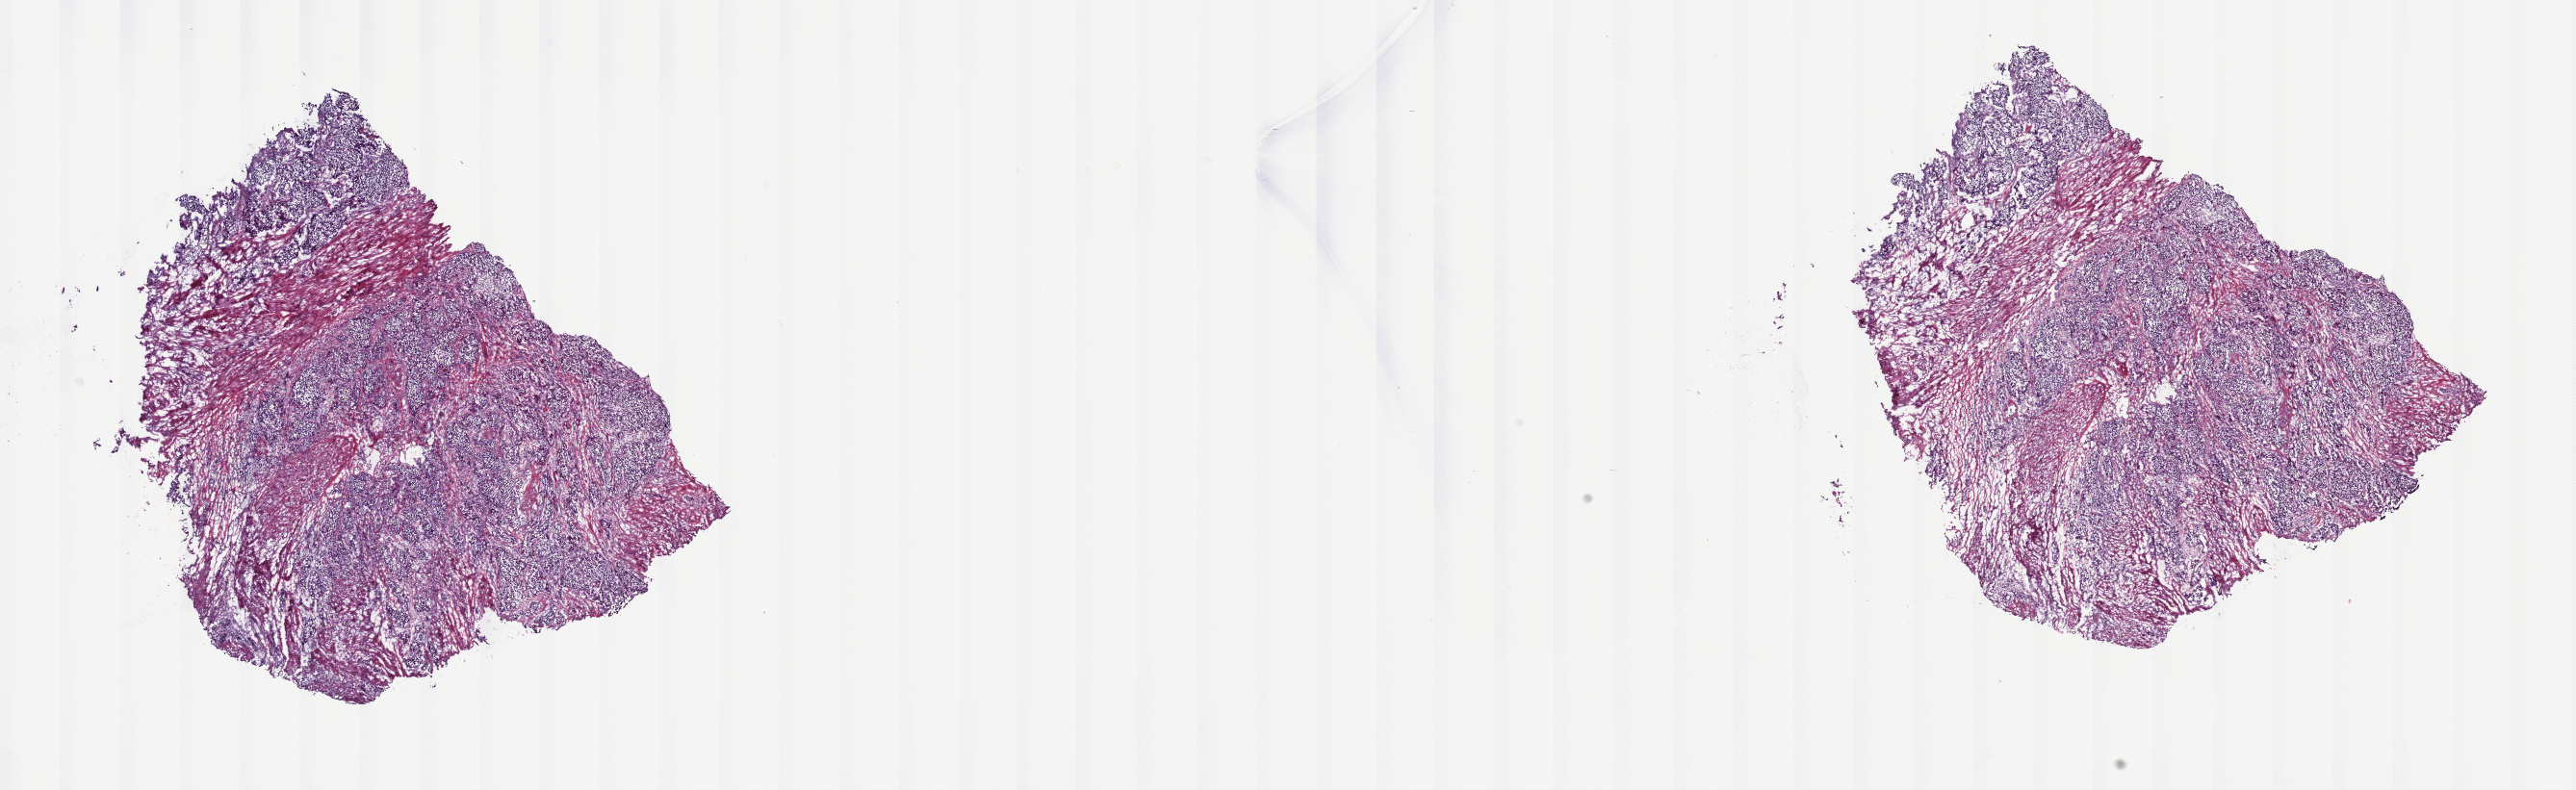
H&E whole-slide image, whole scanned area (about 21.6 x 6.6 mm) shown as a low-resolution overview. Frozen section from the top of the tissue portion. Bladder, primary tumour sample. Male, age 59 years at initial diagnosis. Histologic grade: high grade. Composition of this section per pathologist review: tumour cells 100%, tumour nuclei 65%, normal cells 0%, stromal cells 0%, necrosis 0%. Inflammatory infiltration, as recorded: lymphocyte infiltration 2%, monocyte infiltration 0%, neutrophil infiltration 0%.
Lymph nodes positive (case pathology): 1 of 19 examined. AJCC pathologic stage: IV (7th edition). Pathologic diagnosis: Transitional cell carcinoma.